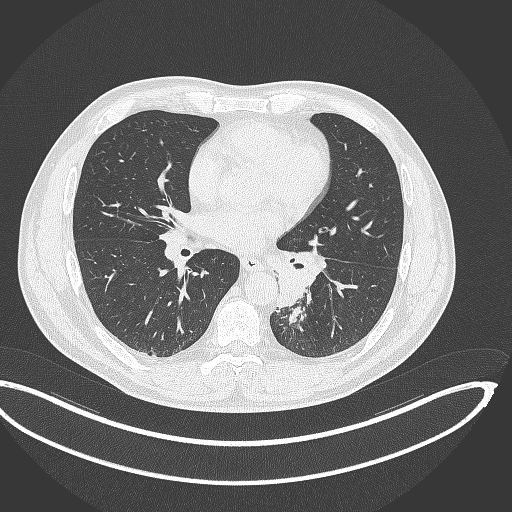
Chest CT, one axial slice. Position 169 of 362 along the scan axis. 120 kVp. Lung window (W 1500 / L -600 HU). 1 mm slice thickness. 512 × 512 image matrix, field of view 442 × 442 mm. Male patient, age 50 years. From the clinical record (not read from this slice): clinical TNM (as recorded): T2a N3 M0.
Outlined on this slice (rectangle marked by the reading radiologist):
- lung tumour (recorded histology: squamous cell carcinoma): box from (x=268, y=245) to (x=327, y=310) px